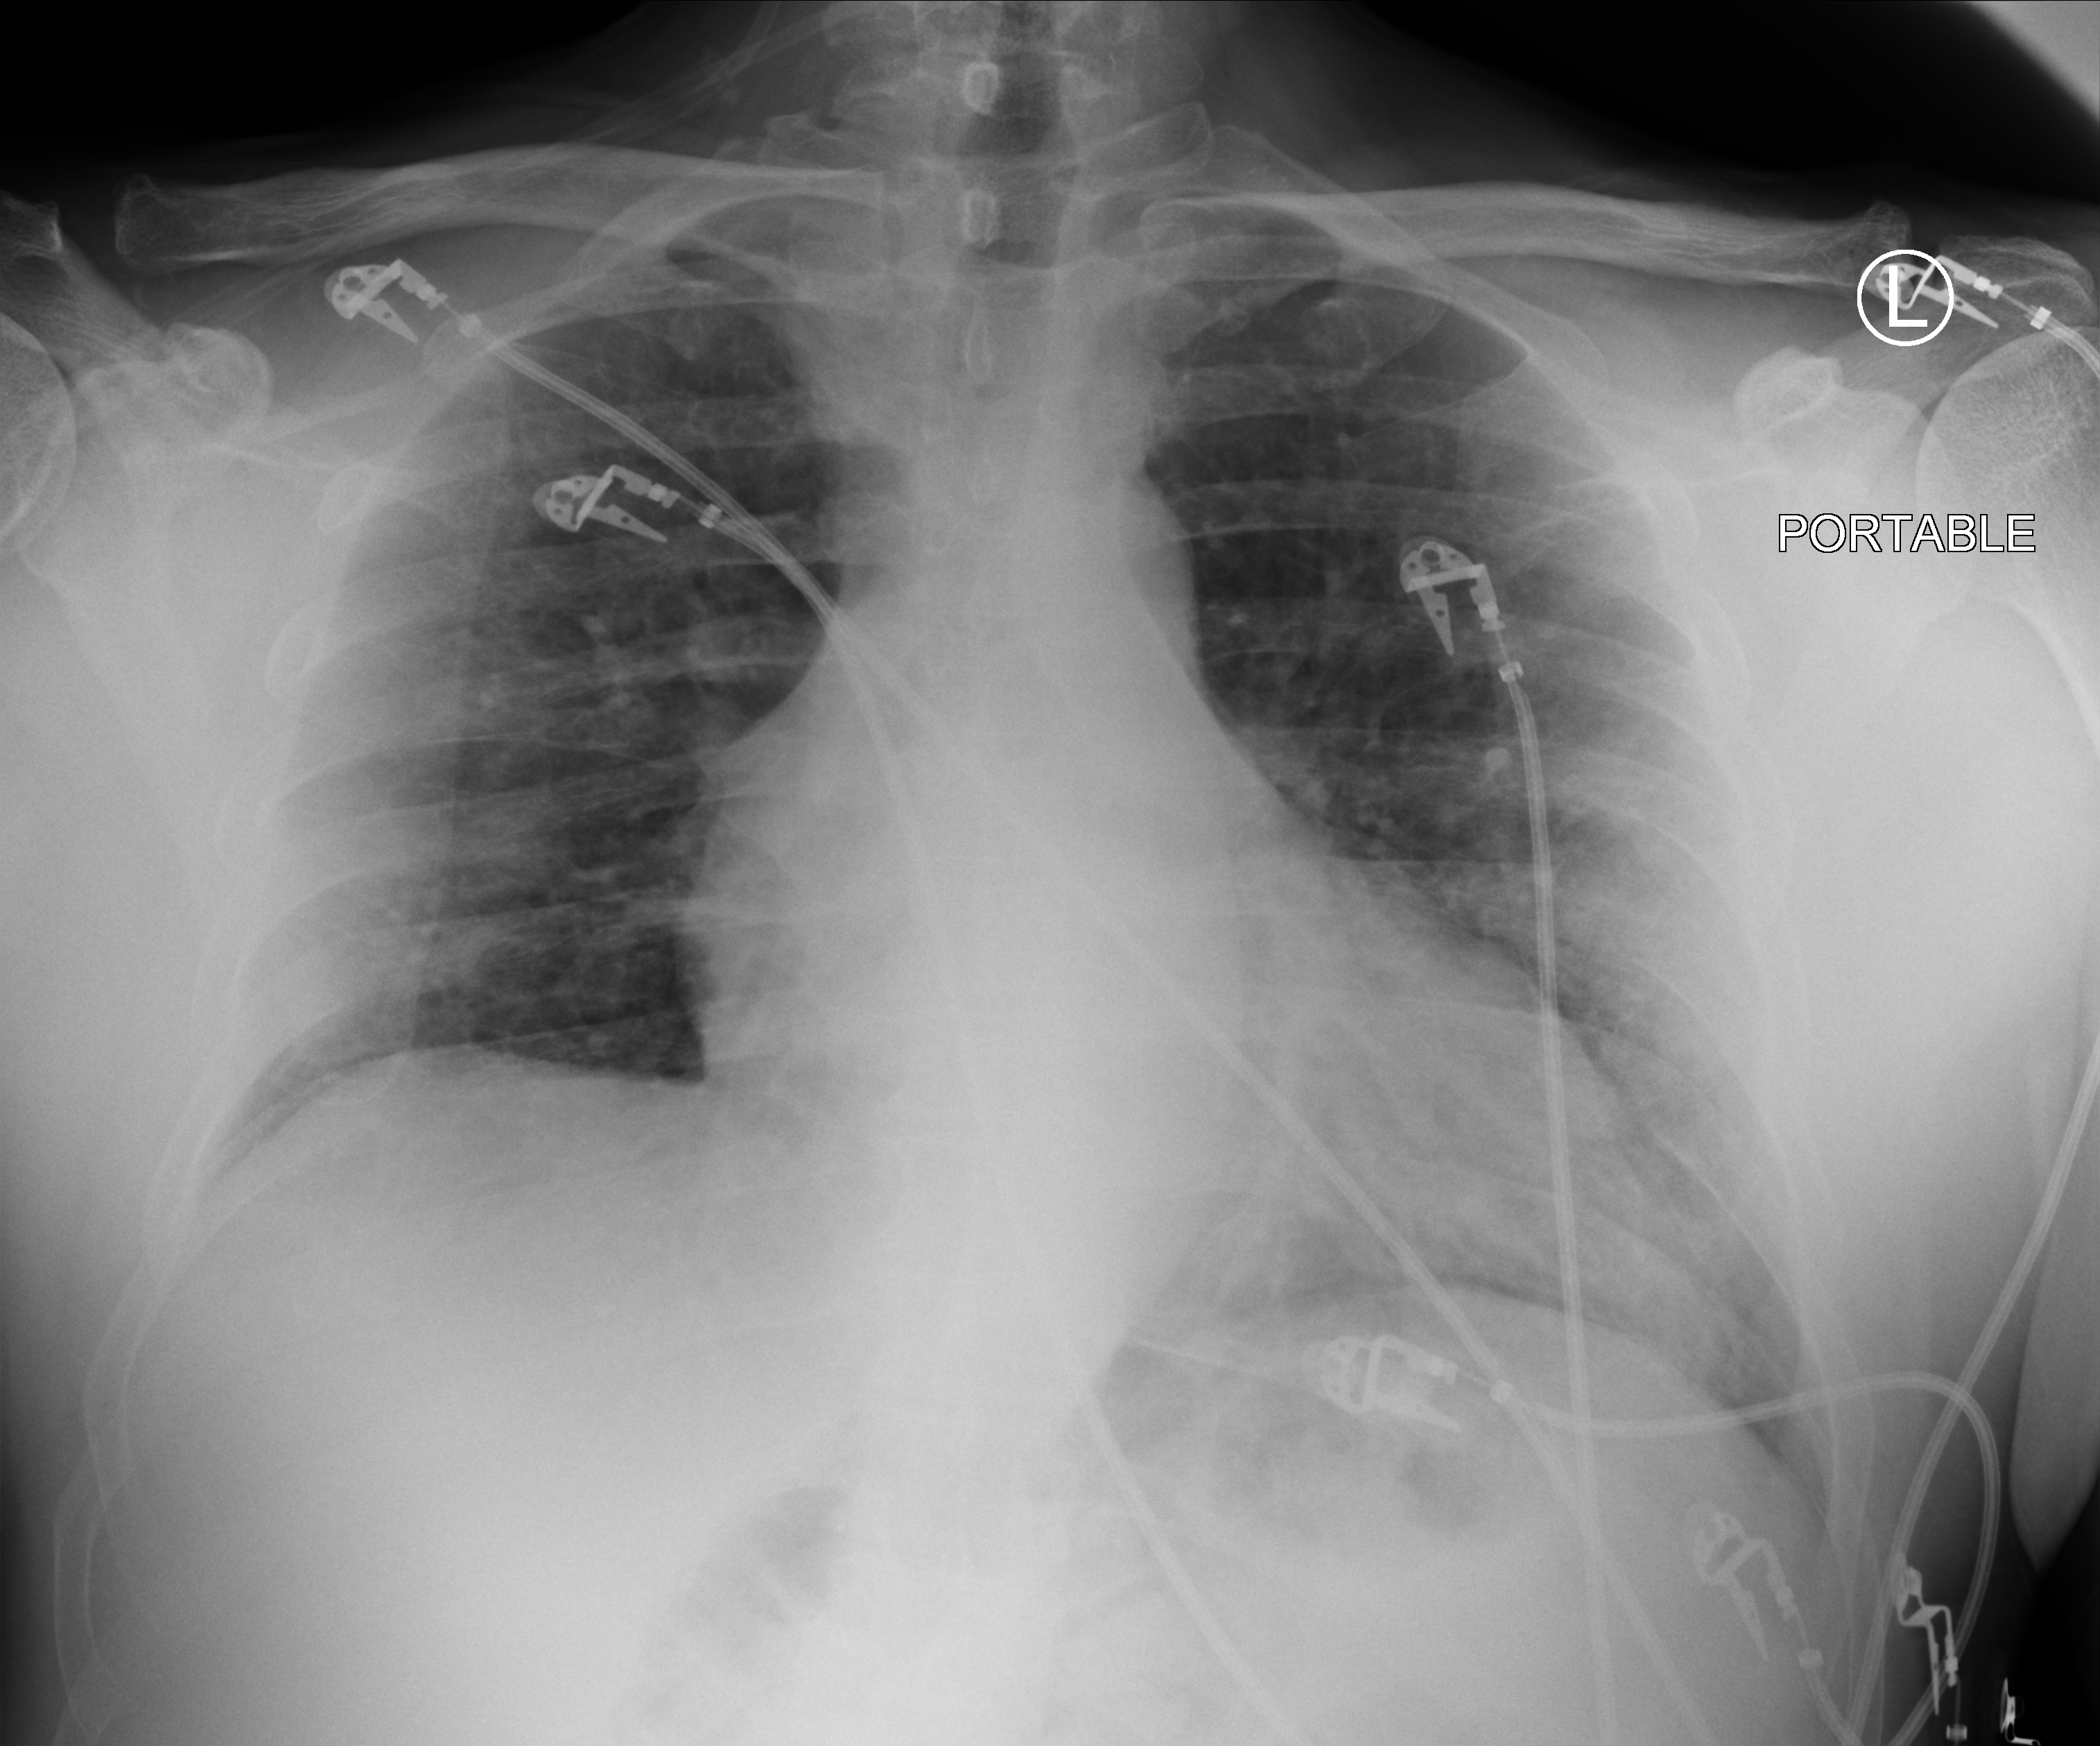
Chest X-ray (portable). Male patient hospitalised with COVID-19, age 18–59 years.
Hospital-stay facts (about this admission, not read from this image; timing relative to this image not recorded): mechanically ventilated during this hospital stay: no; admitted to intensive care during this hospital stay: no.